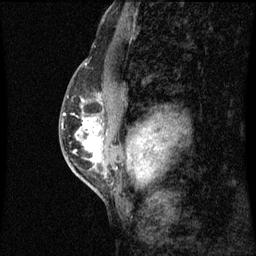
Breast MRI (dynamic contrast-enhanced), one sagittal slice; dynamic contrast-enhanced series, image 2 of 3 at this slice position (ordered by acquisition); 1.5 T; TE 4.2 ms, TR 8.9 ms; 2 mm slice thickness; 256 × 256 image matrix, field of view 200 × 200 mm. Female patient, age 50 years. From the clinical record (not read from this slice): setting: breast cancer imaged before/during neoadjuvant chemotherapy; receptor status: triple-negative.
Outlined on this slice (semi-automatically segmented with operator editing):
- analysis volume of interest (the breast-tissue region the enhancement analysis was run in; not a lesion): bounding box (x1, y1, x2, y2) in pixels: (68, 80, 104, 169)
- tumour enhancement mask (voxels above the 70 % enhancement threshold inside the analysis volume of interest): (75, 120, 101, 163)